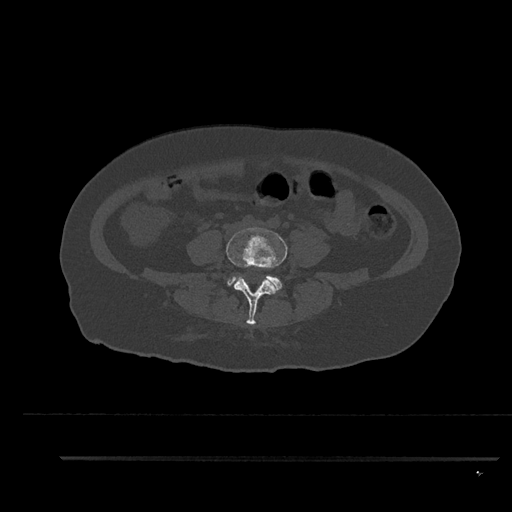
CT including the spine, one axial slice; position 2 of 797 along the scan axis; reconstruction kernel Br40s/3; 120 kVp; bone window (W 1800 / L 400 HU); 0.5 mm slice thickness; 512 × 512 image matrix, field of view 408 × 408 mm. Patient: female, 44 years. Case-level facts recorded for this patient, not image findings: primary cancer: renal; vertebrae with lytic lesions (as recorded): L1.
Structures marked on this image (semi-automatically segmented with operator editing):
- L4 vertebra: bounding box [x1, y1, x2, y2] px = [226, 227, 288, 325]